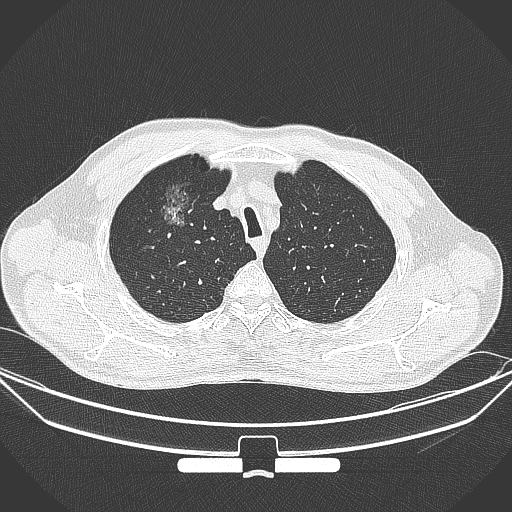
Chest CT, one axial slice; position 286 of 355 along the scan axis; 120 kVp; lung window (W 1500 / L -600 HU); 1 mm slice thickness; 512 × 512 image matrix. Patient: male, 67 years. From the clinical record (not read from this slice): clinical TNM (as recorded): T1c N0 M0.
Outlined on this slice (rectangle marked by the reading radiologist):
- lung tumour (recorded histology: adenocarcinoma): bounding box <148,173,207,243> (left, top, right, bottom; pixels)